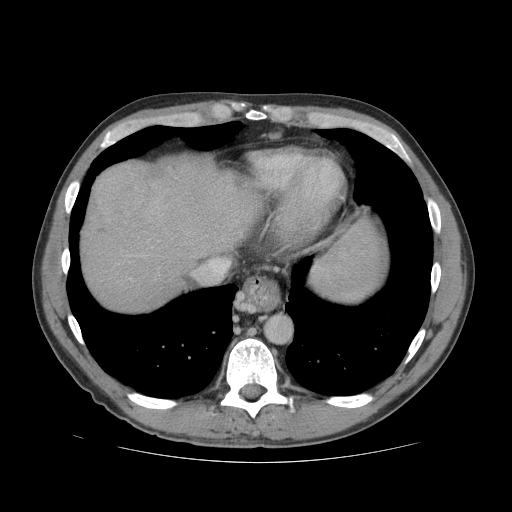
Contrast-enhanced abdominal CT (liver protocol), one axial slice; position 67 of 81 along the scan axis; reconstruction kernel STANDARD; 140 kVp; soft-tissue window (W 400 / L 40 HU); 2.5 mm slice thickness; 512 × 512 image matrix, field of view 400 × 400 mm. Case-level facts recorded for this patient, not image findings: diagnosis: hepatocellular carcinoma (patient treated with transarterial chemoembolisation; whether this scan precedes or follows treatment is not stated here); TNM stage (as recorded): Stage-IVB; Child-Pugh class: B; tumour differentiation: well differentiated.
Outlined on this slice (semi-automatically segmented with operator editing):
- liver parenchyma outside the tumour (the mass and vessels are separate outlines, so this box may not span the whole liver): bounding box <80,159,254,312> (left, top, right, bottom; pixels)
- mass: <94,160,150,216>